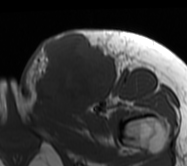
MRI of an extremity soft-tissue mass, one axial slice; position 26 of 62 along the scan axis; MR volume resampled by the dataset authors to the PET/CT grid (not the native acquisition matrix); 187 × 166 image matrix, field of view 183 × 162 mm. Female patient. Case-level facts recorded for this patient, not image findings: histological type: leiomyosarcoma; grade: high; site of the primary tumour: groin.
Annotated regions visible in this slice (expert contour drawn on MRI and transferred to this co-registered scan by the dataset authors):
- gross tumour volume including surrounding oedema: box from (x=20, y=30) to (x=133, y=114) px
- gross tumour volume (mass): (x=34, y=33)–(x=115, y=111)